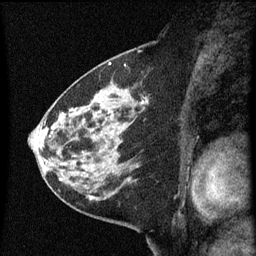
Breast MRI (dynamic contrast-enhanced), one sagittal slice; slice 31 of 60 in the series (ordered by position); dynamic contrast-enhanced series, image 2 of 3 at this slice position (ordered by acquisition); 1.5 T; TE 4.2 ms, TR 8 ms; 2 mm slice thickness; 256 × 256 image matrix, field of view 180 × 180 mm. Patient: female, 60 years.
Structures marked on this image (semi-automatically segmented with operator editing):
- analysis volume of interest (the breast-tissue region the enhancement analysis was run in; not a lesion): bounding box <48,82,151,183> (left, top, right, bottom; pixels)
- tumour enhancement mask (voxels above the 70 % enhancement threshold inside the analysis volume of interest): <51,102,148,181>